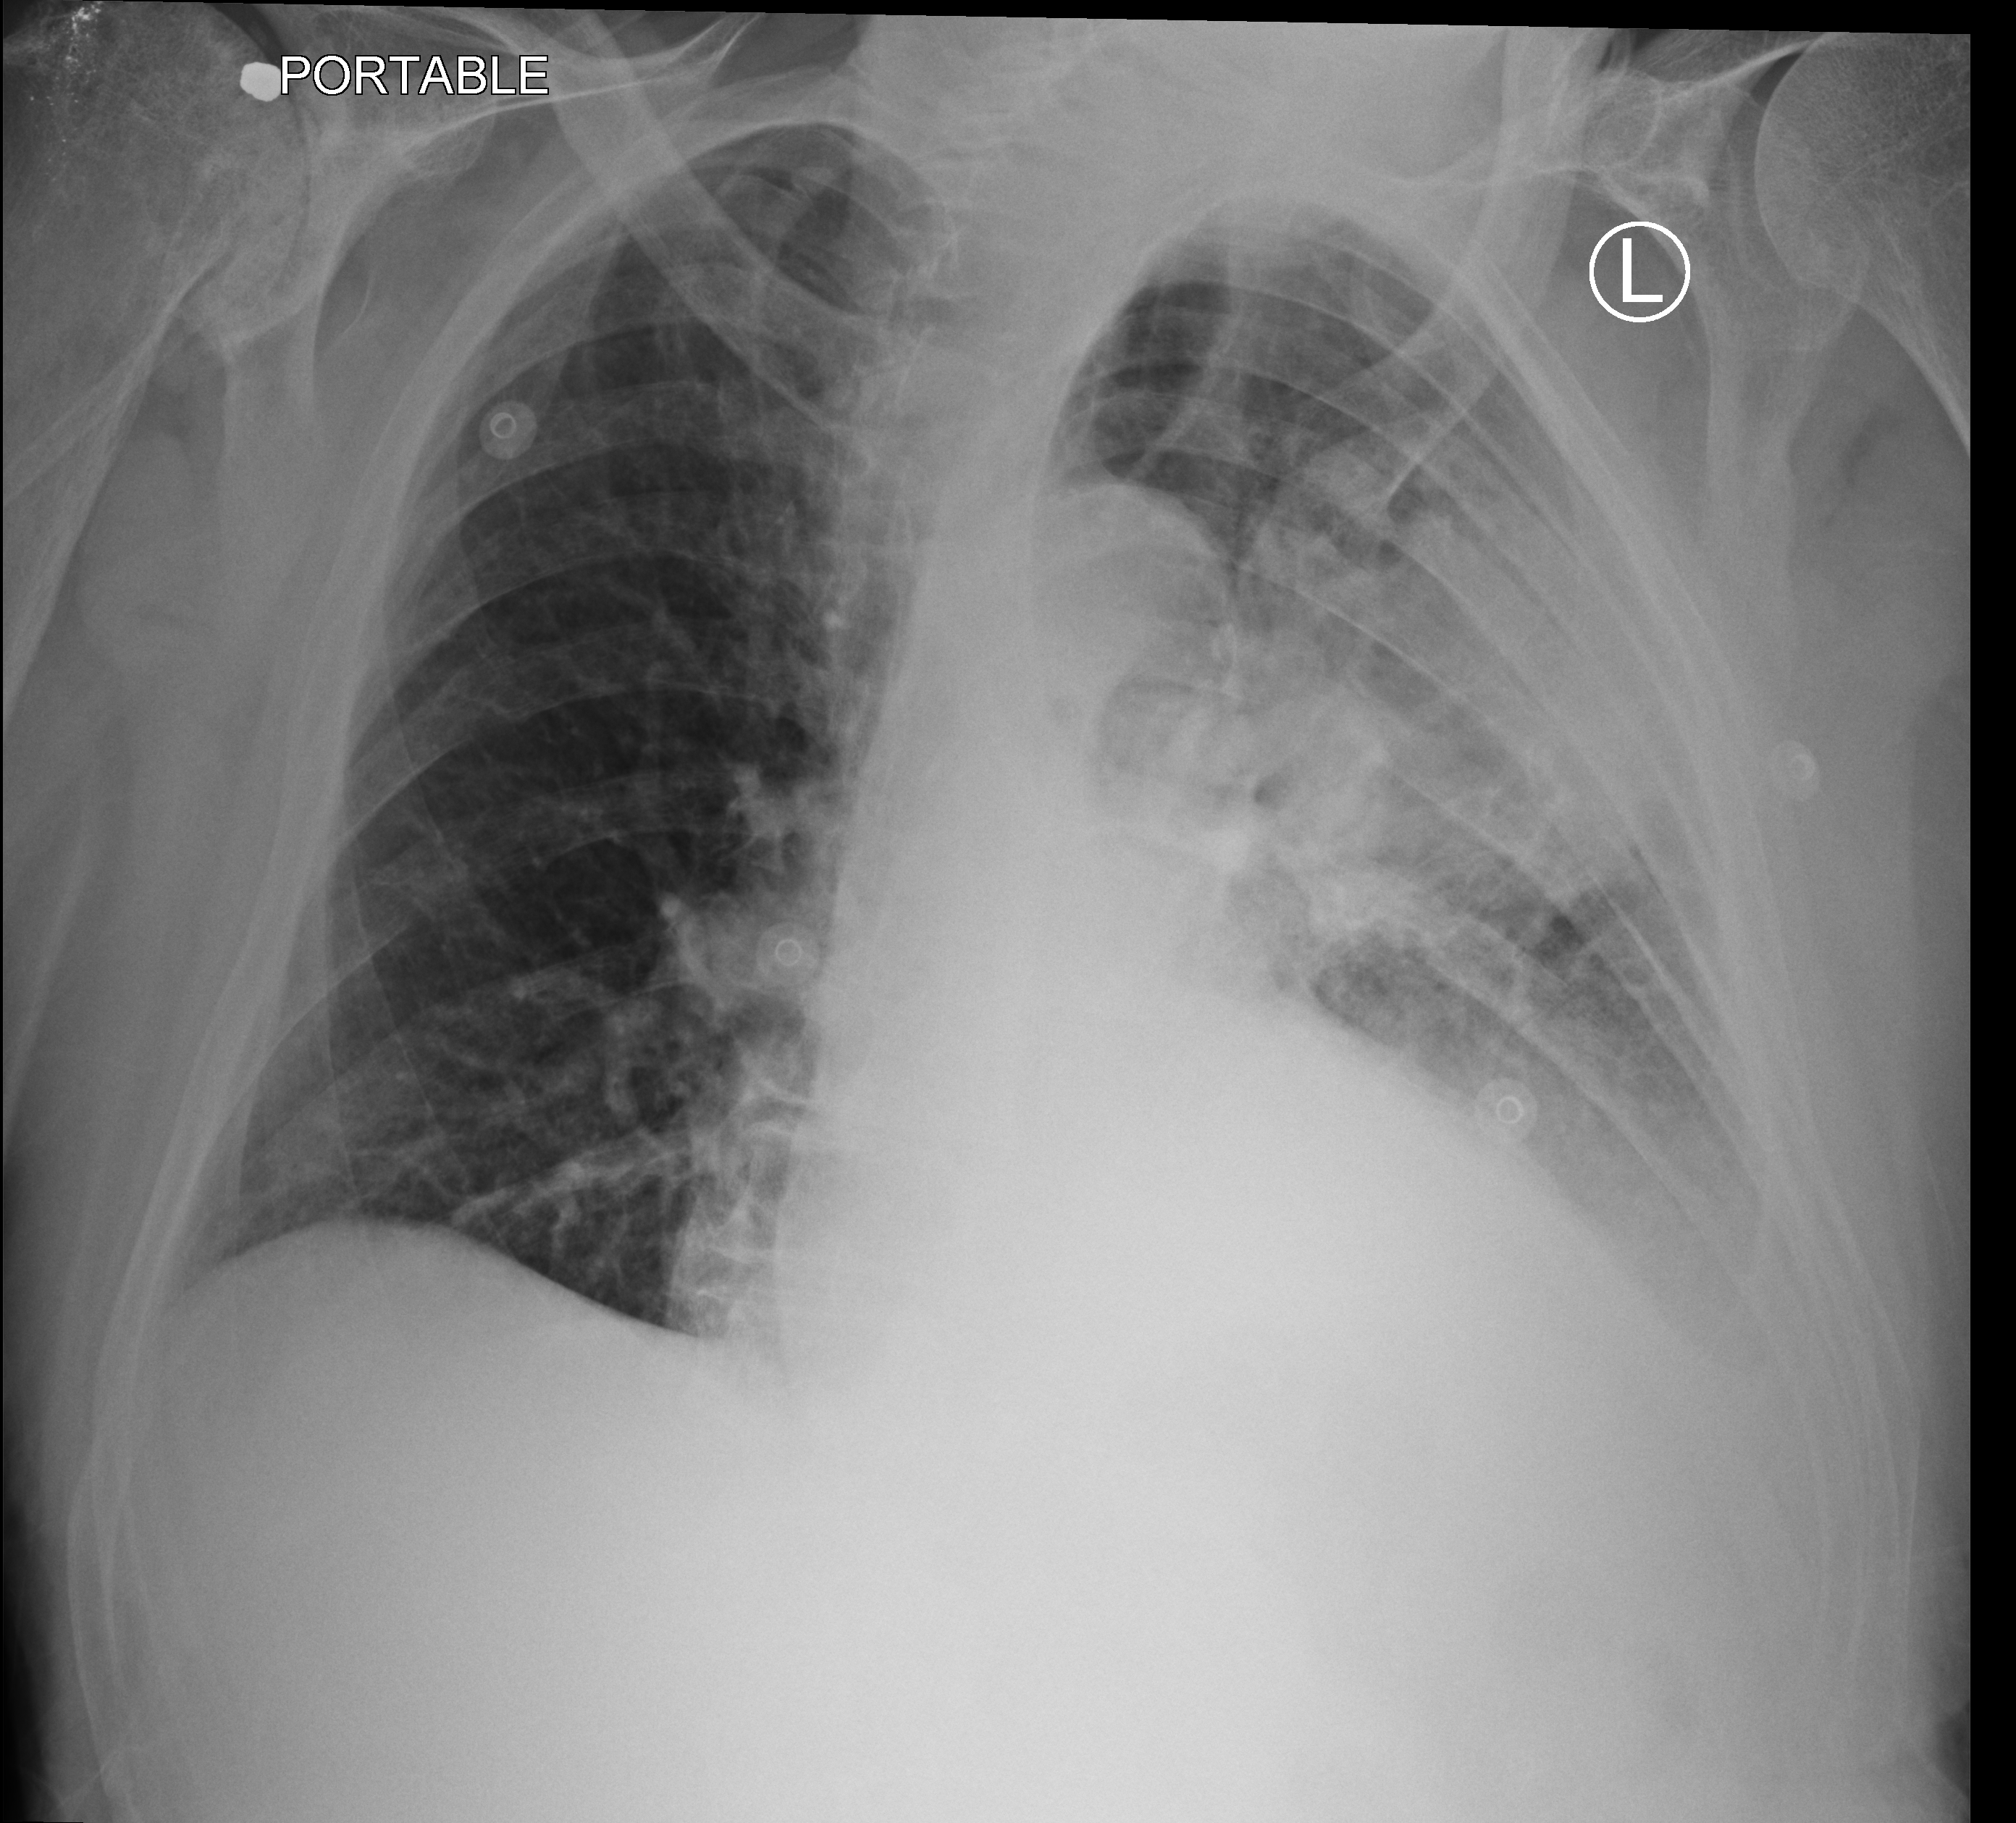
Bedside chest radiograph (computed radiography), anteroposterior (AP) projection. Male patient hospitalised with COVID-19, age 75–90 years.
Admission-level facts for this patient (not findings on this image; timing relative to this image not recorded):
- smoking status (admission record): former
- mechanically ventilated during this hospital stay: no